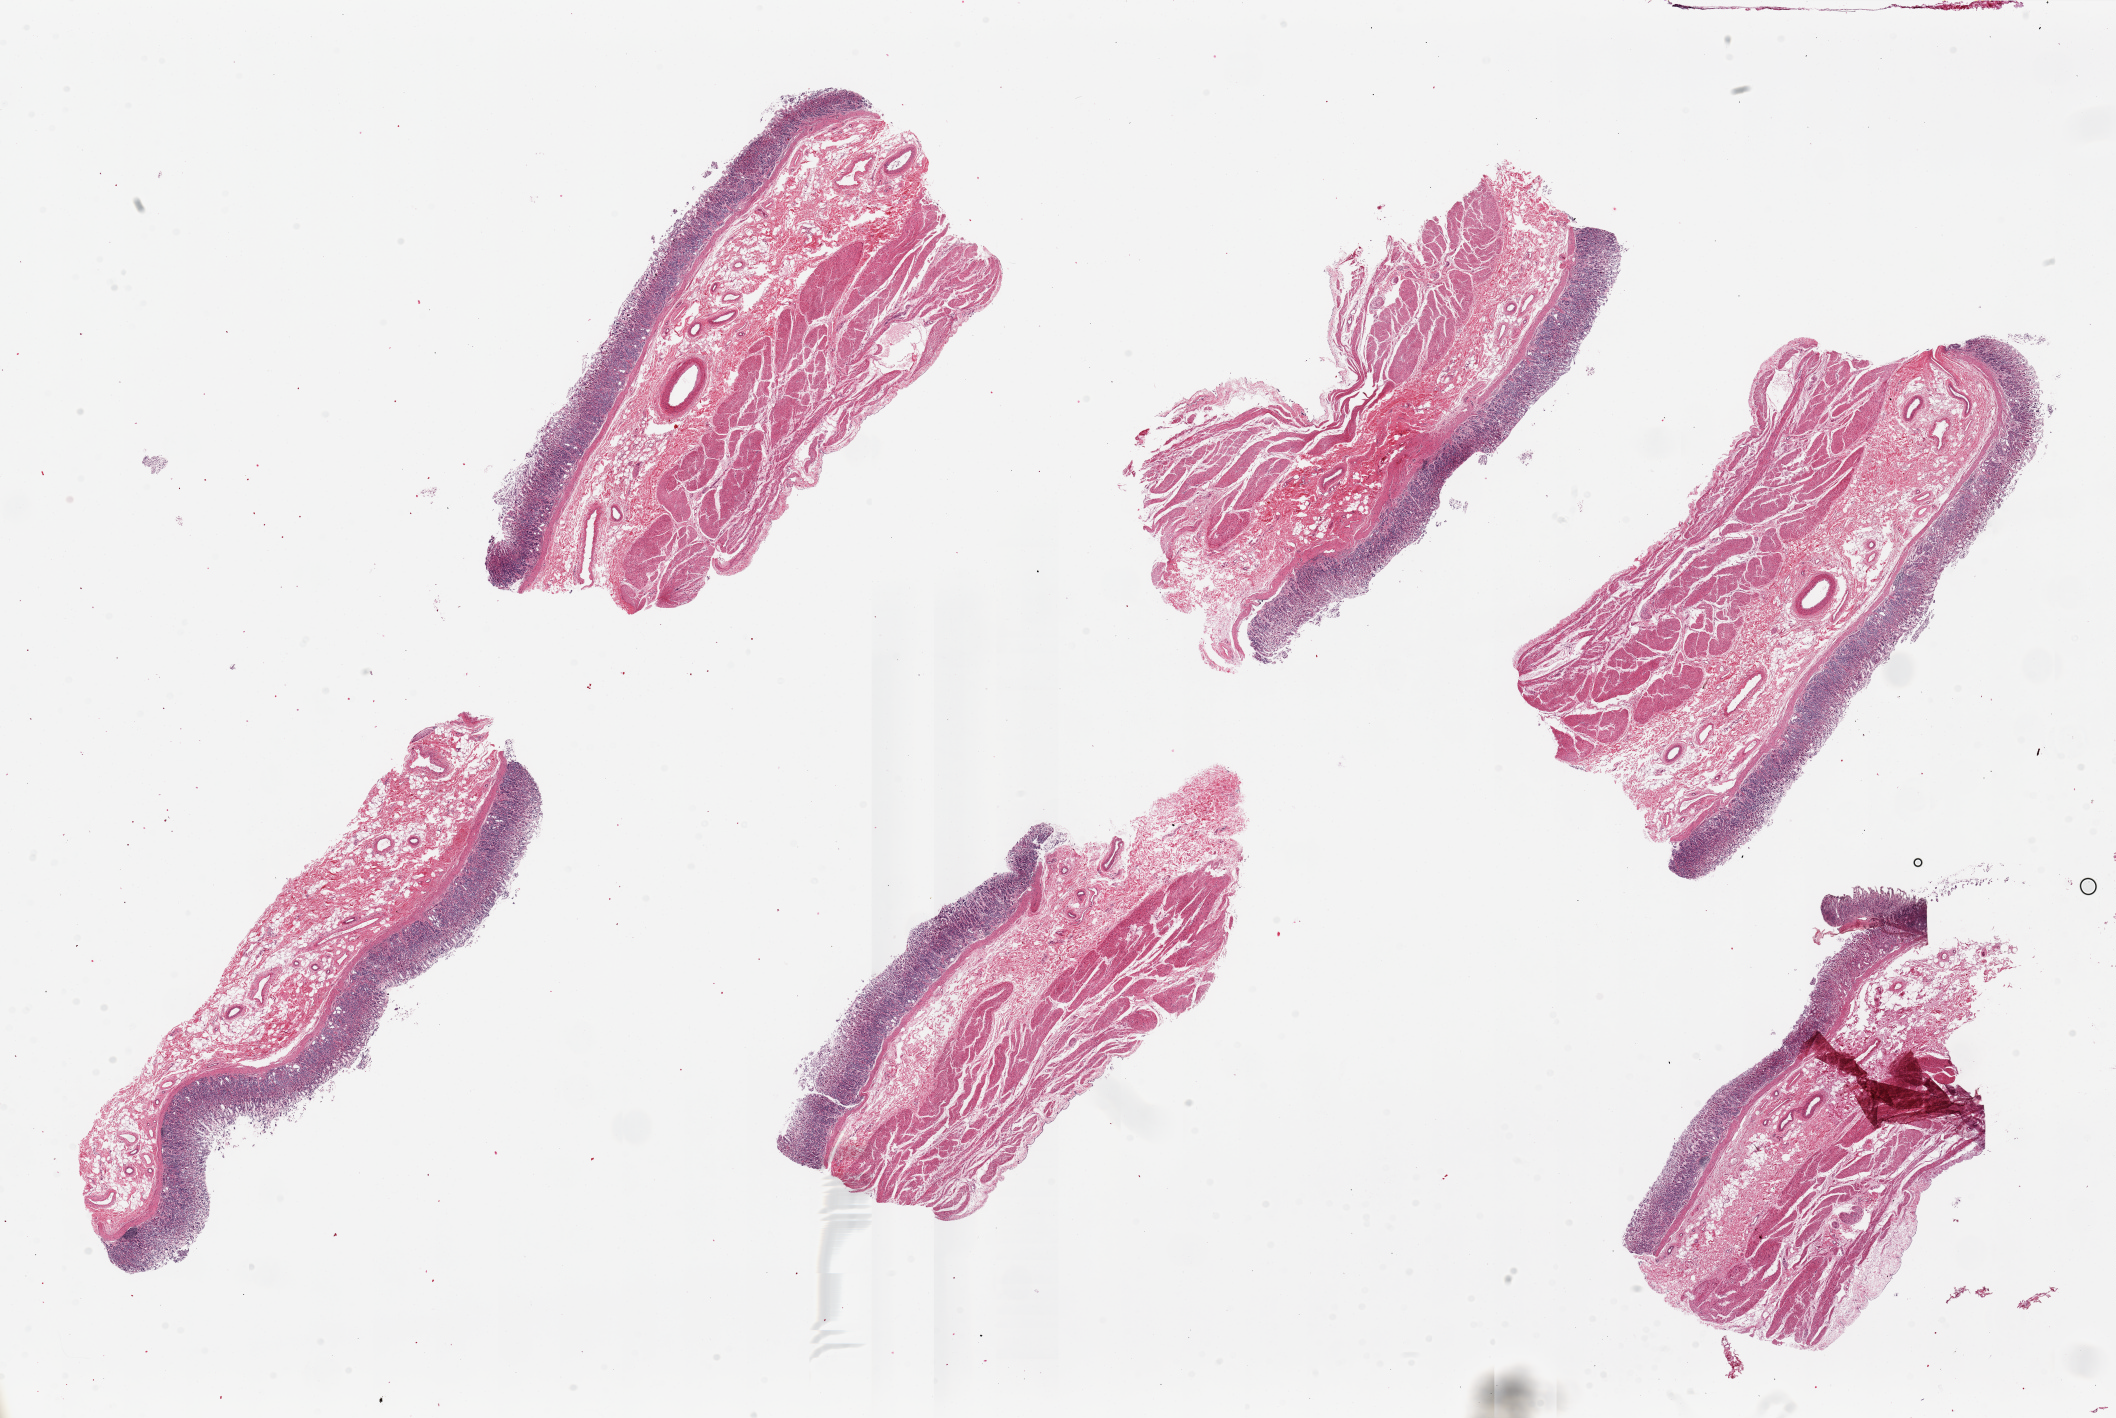
Whole-slide image, hematoxylin and eosin (H&E) stain — low-resolution overview of the scanned area, about 33.5 x 22.4 mm; PAXgene-fixed paraffin-embedded (PFPE) section; target tissue: stomach; tissue donor sample.
Review note (as recorded): 6 pieces, up to 11x3mm; mucosa ~10-15% thickness, mild/moderate autolysis.